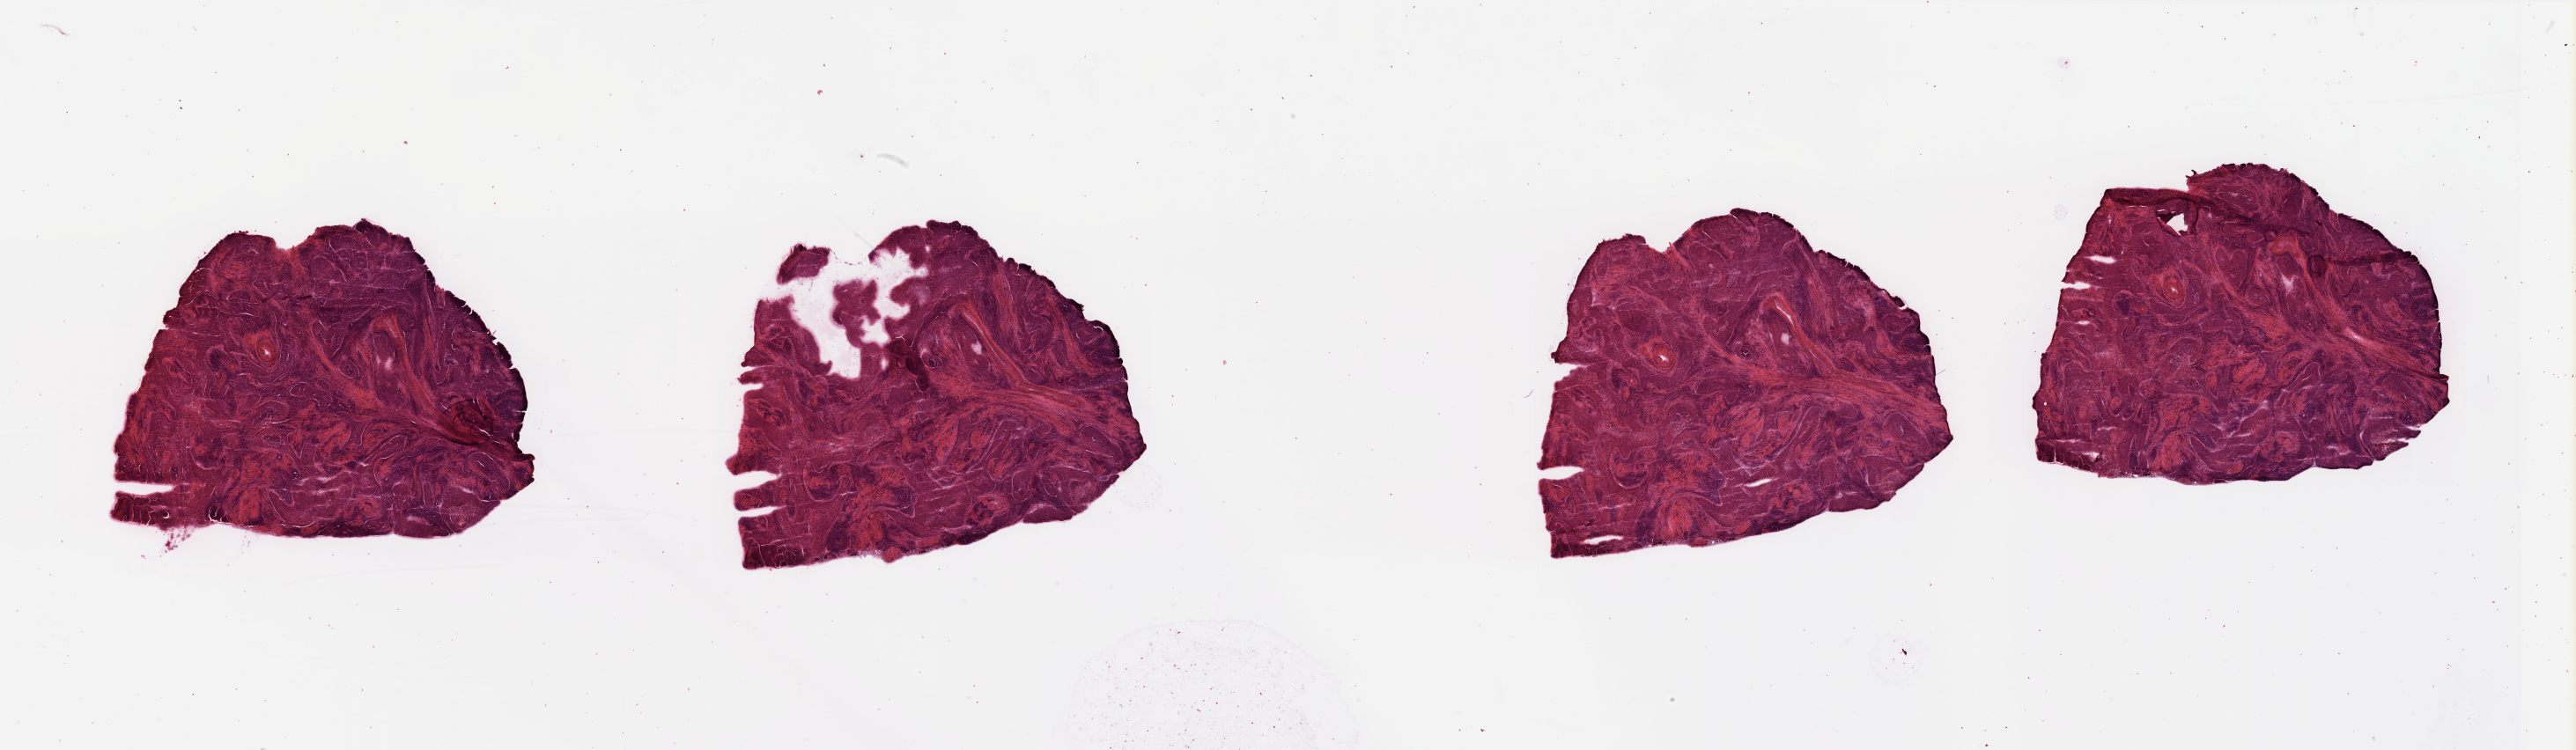
Whole-slide histology image, H&E, shown as a low-resolution overview of the whole scanned area (about 46.3 x 13.5 mm), head and neck, tissue type not recorded. Male, 67 y/o.
Patient diagnosis: Squamous cell carcinoma, NOS (larynx, NOS).